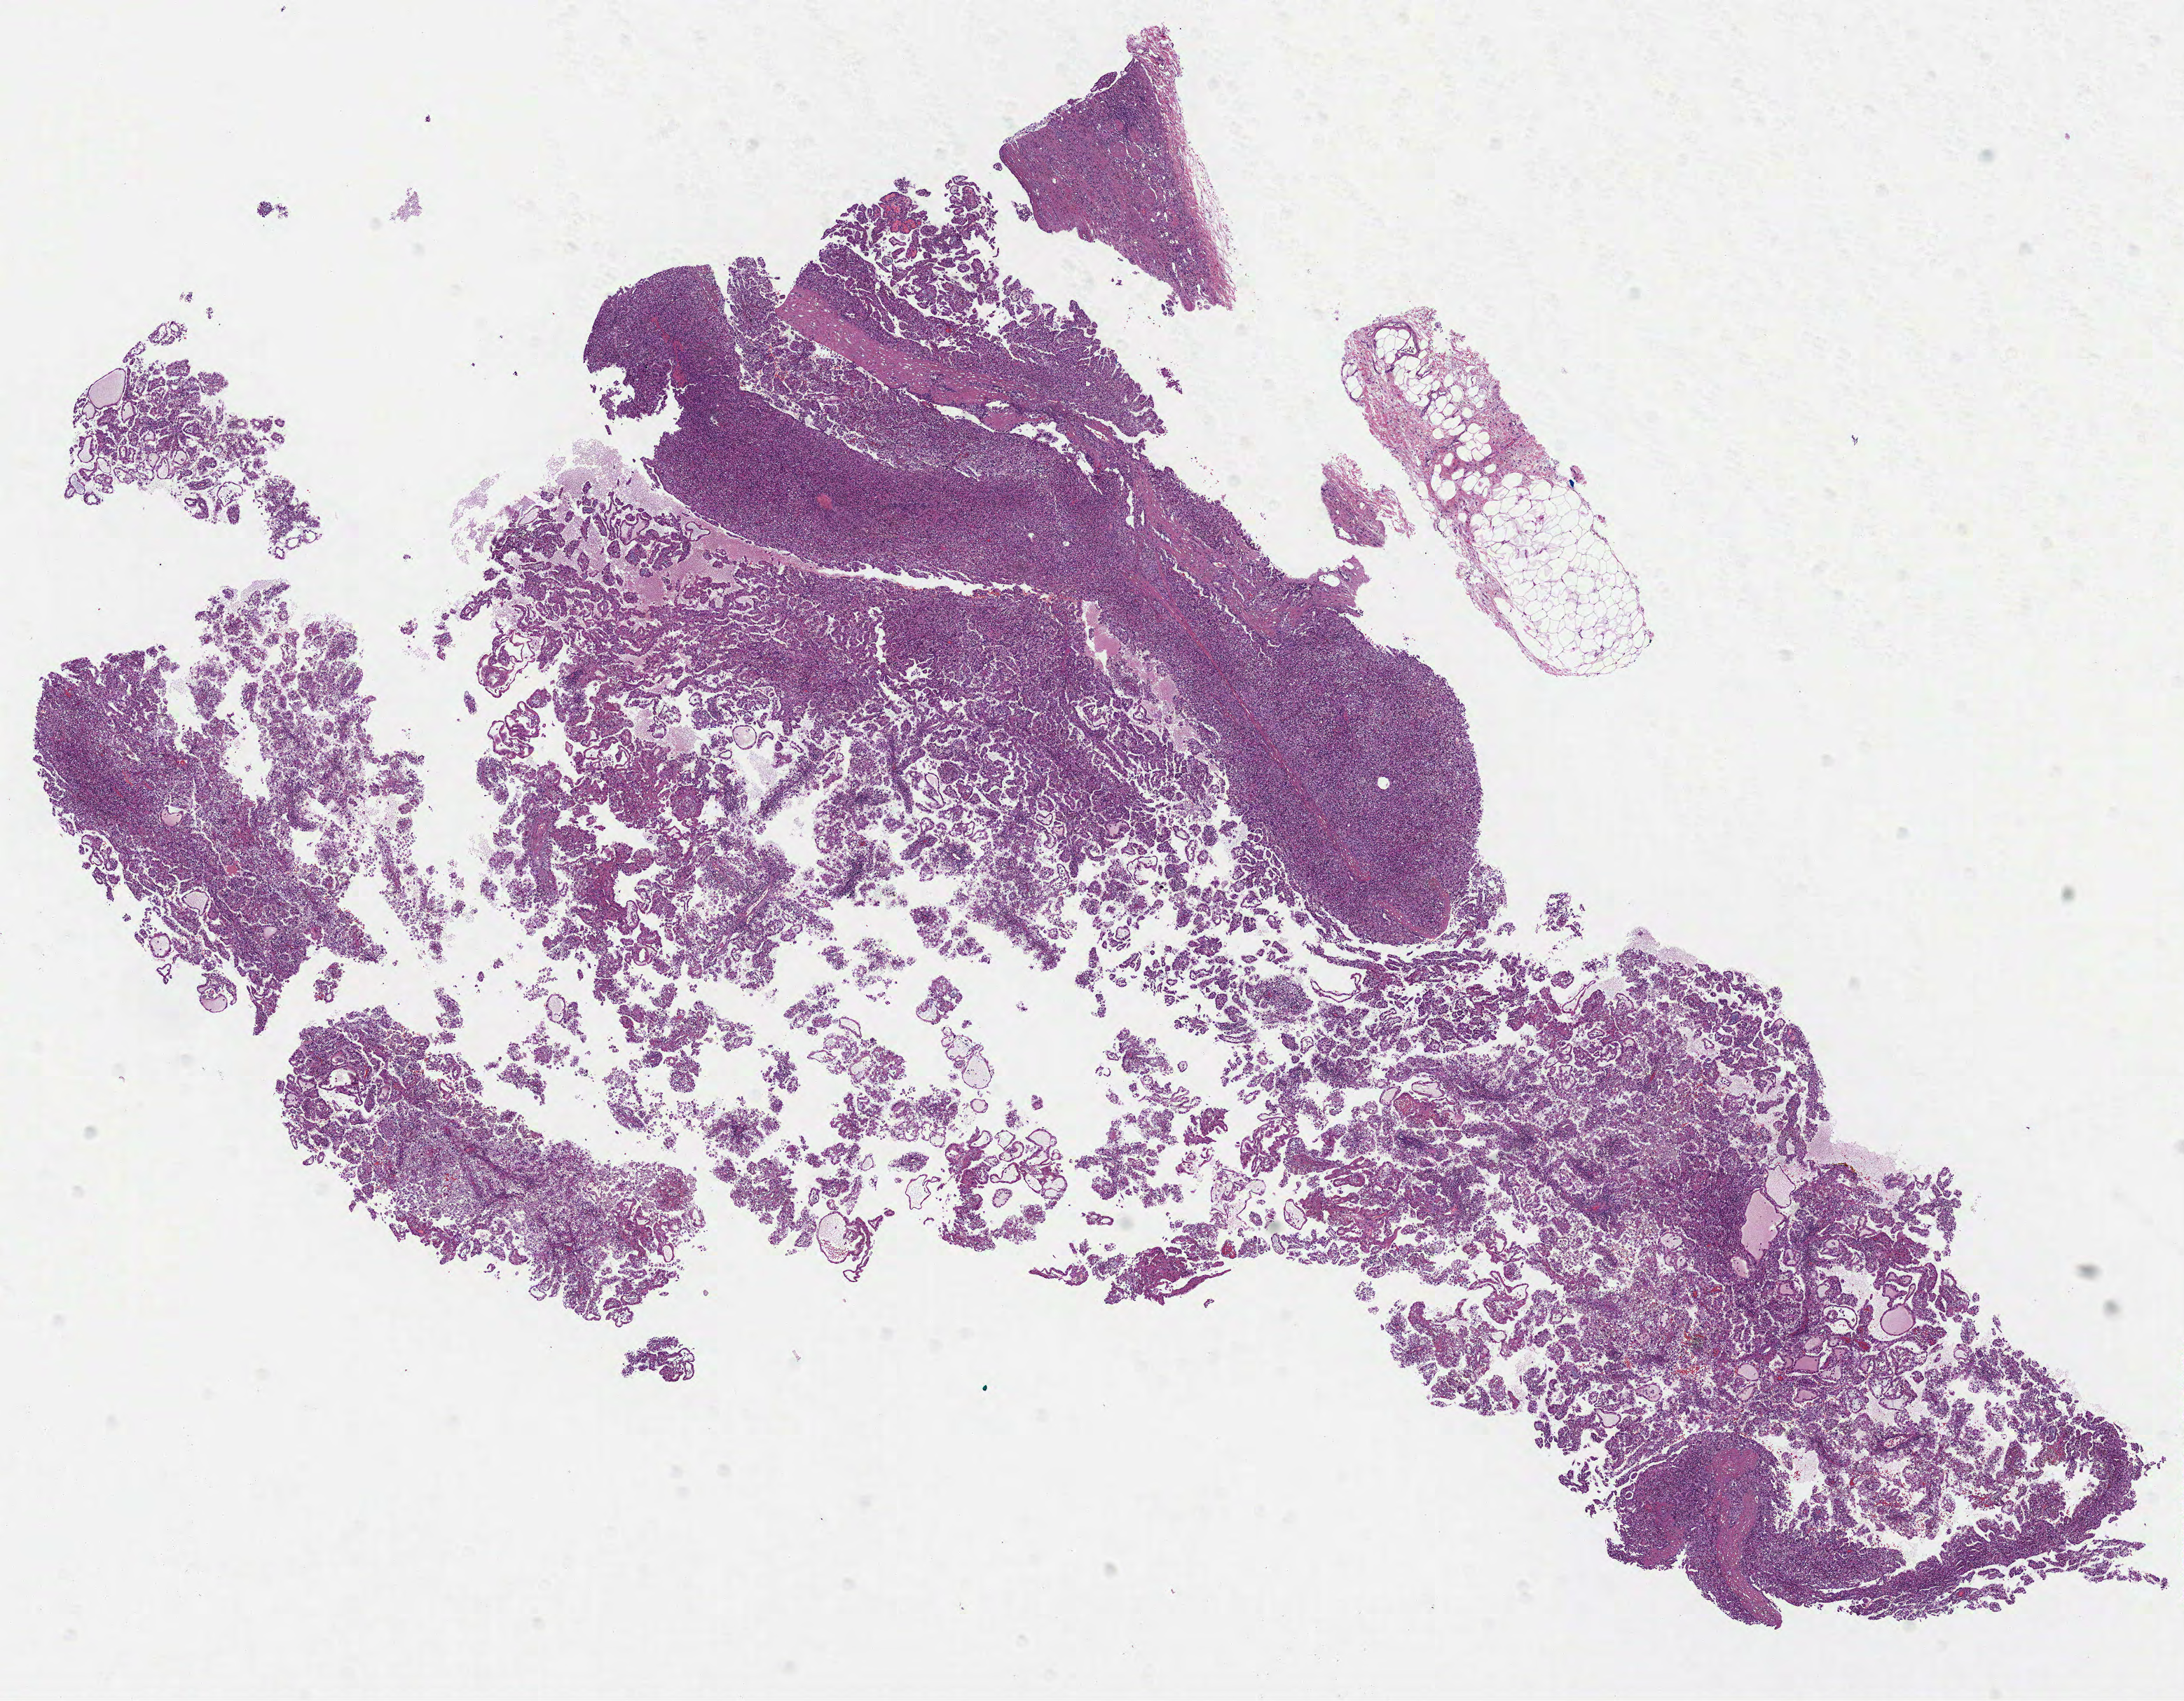
Whole-slide histology image, H&E — low-resolution overview of the scanned area, about 12.6 x 9.8 mm (slide scanned at 40x); formalin-fixed paraffin-embedded (FFPE) diagnostic section; primary tumour sample from the kidney. Female, age 61 years at initial diagnosis.
AJCC pathologic stage: I (7th edition). Laterality: left. Diagnosis: Papillary adenocarcinoma, NOS.